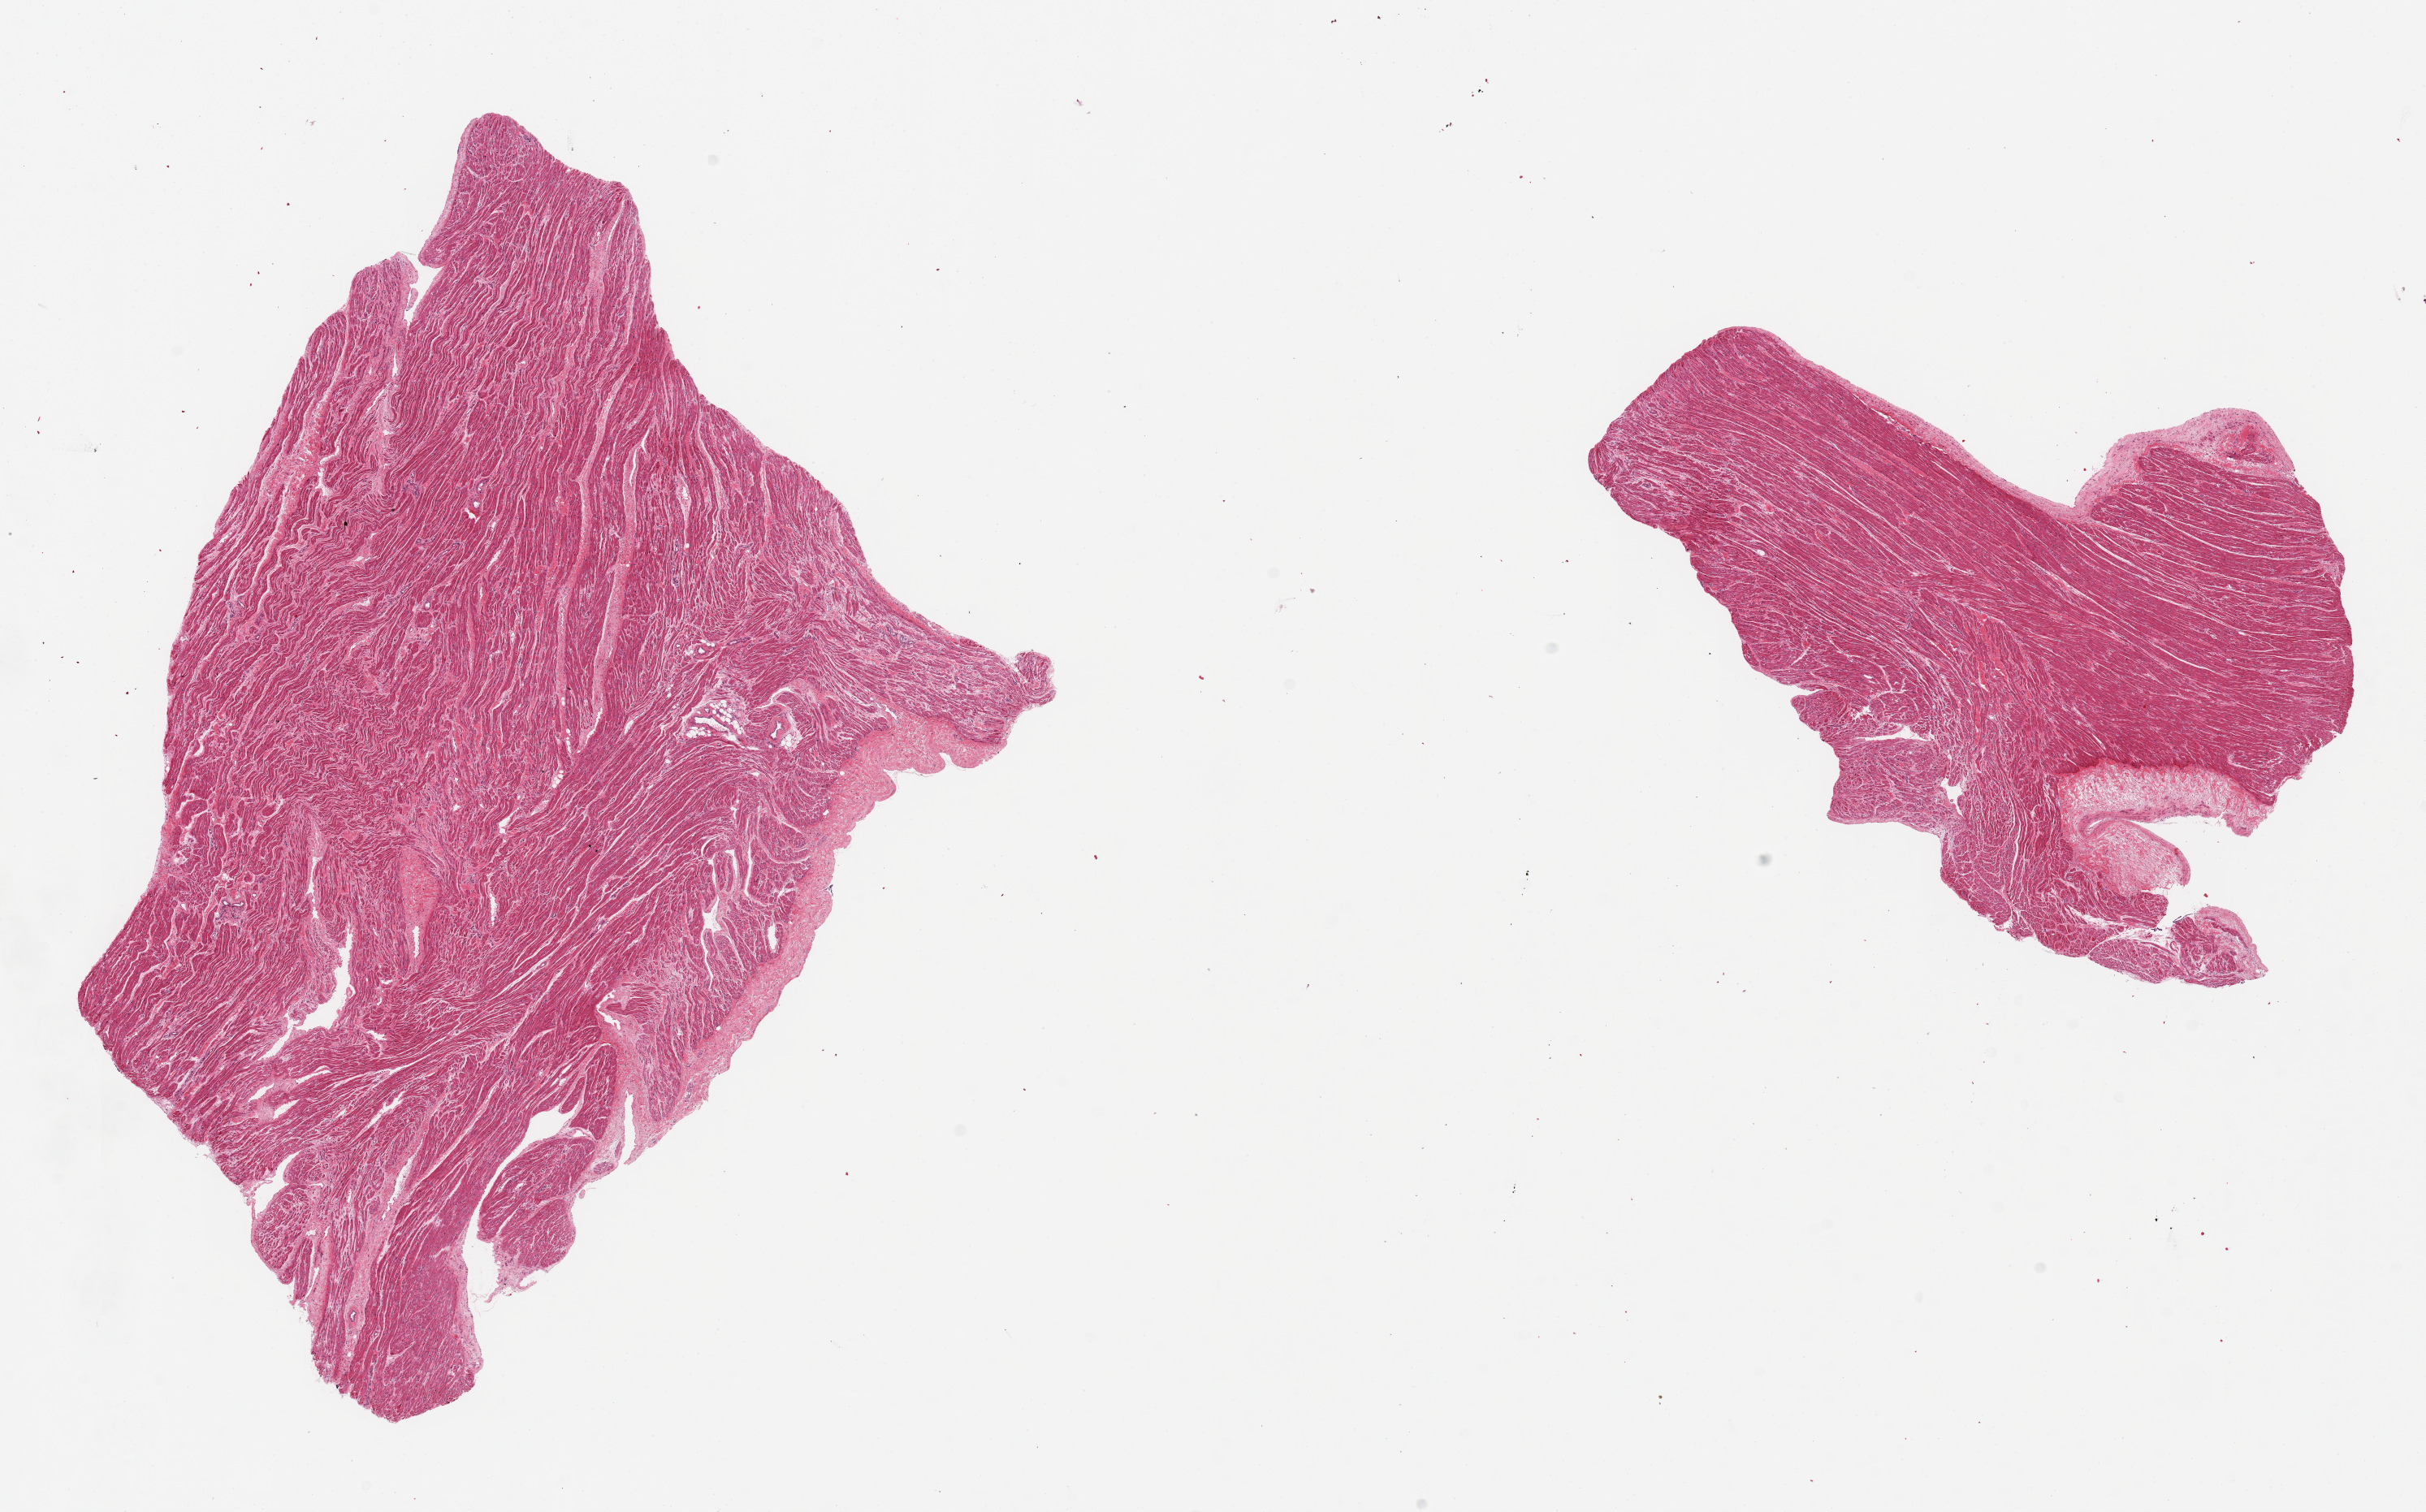
Digitized H&E-stained section, whole scanned area (about 23.6 x 14.7 mm, acquisition: 20x scan) shown as a low-resolution overview. PAXgene-fixed paraffin-embedded (PFPE) section. Sampled site (target tissue): auricular appendage. Tissue donor sample. Donor: female.
* pathologist's review note for this sample: 2 pieces